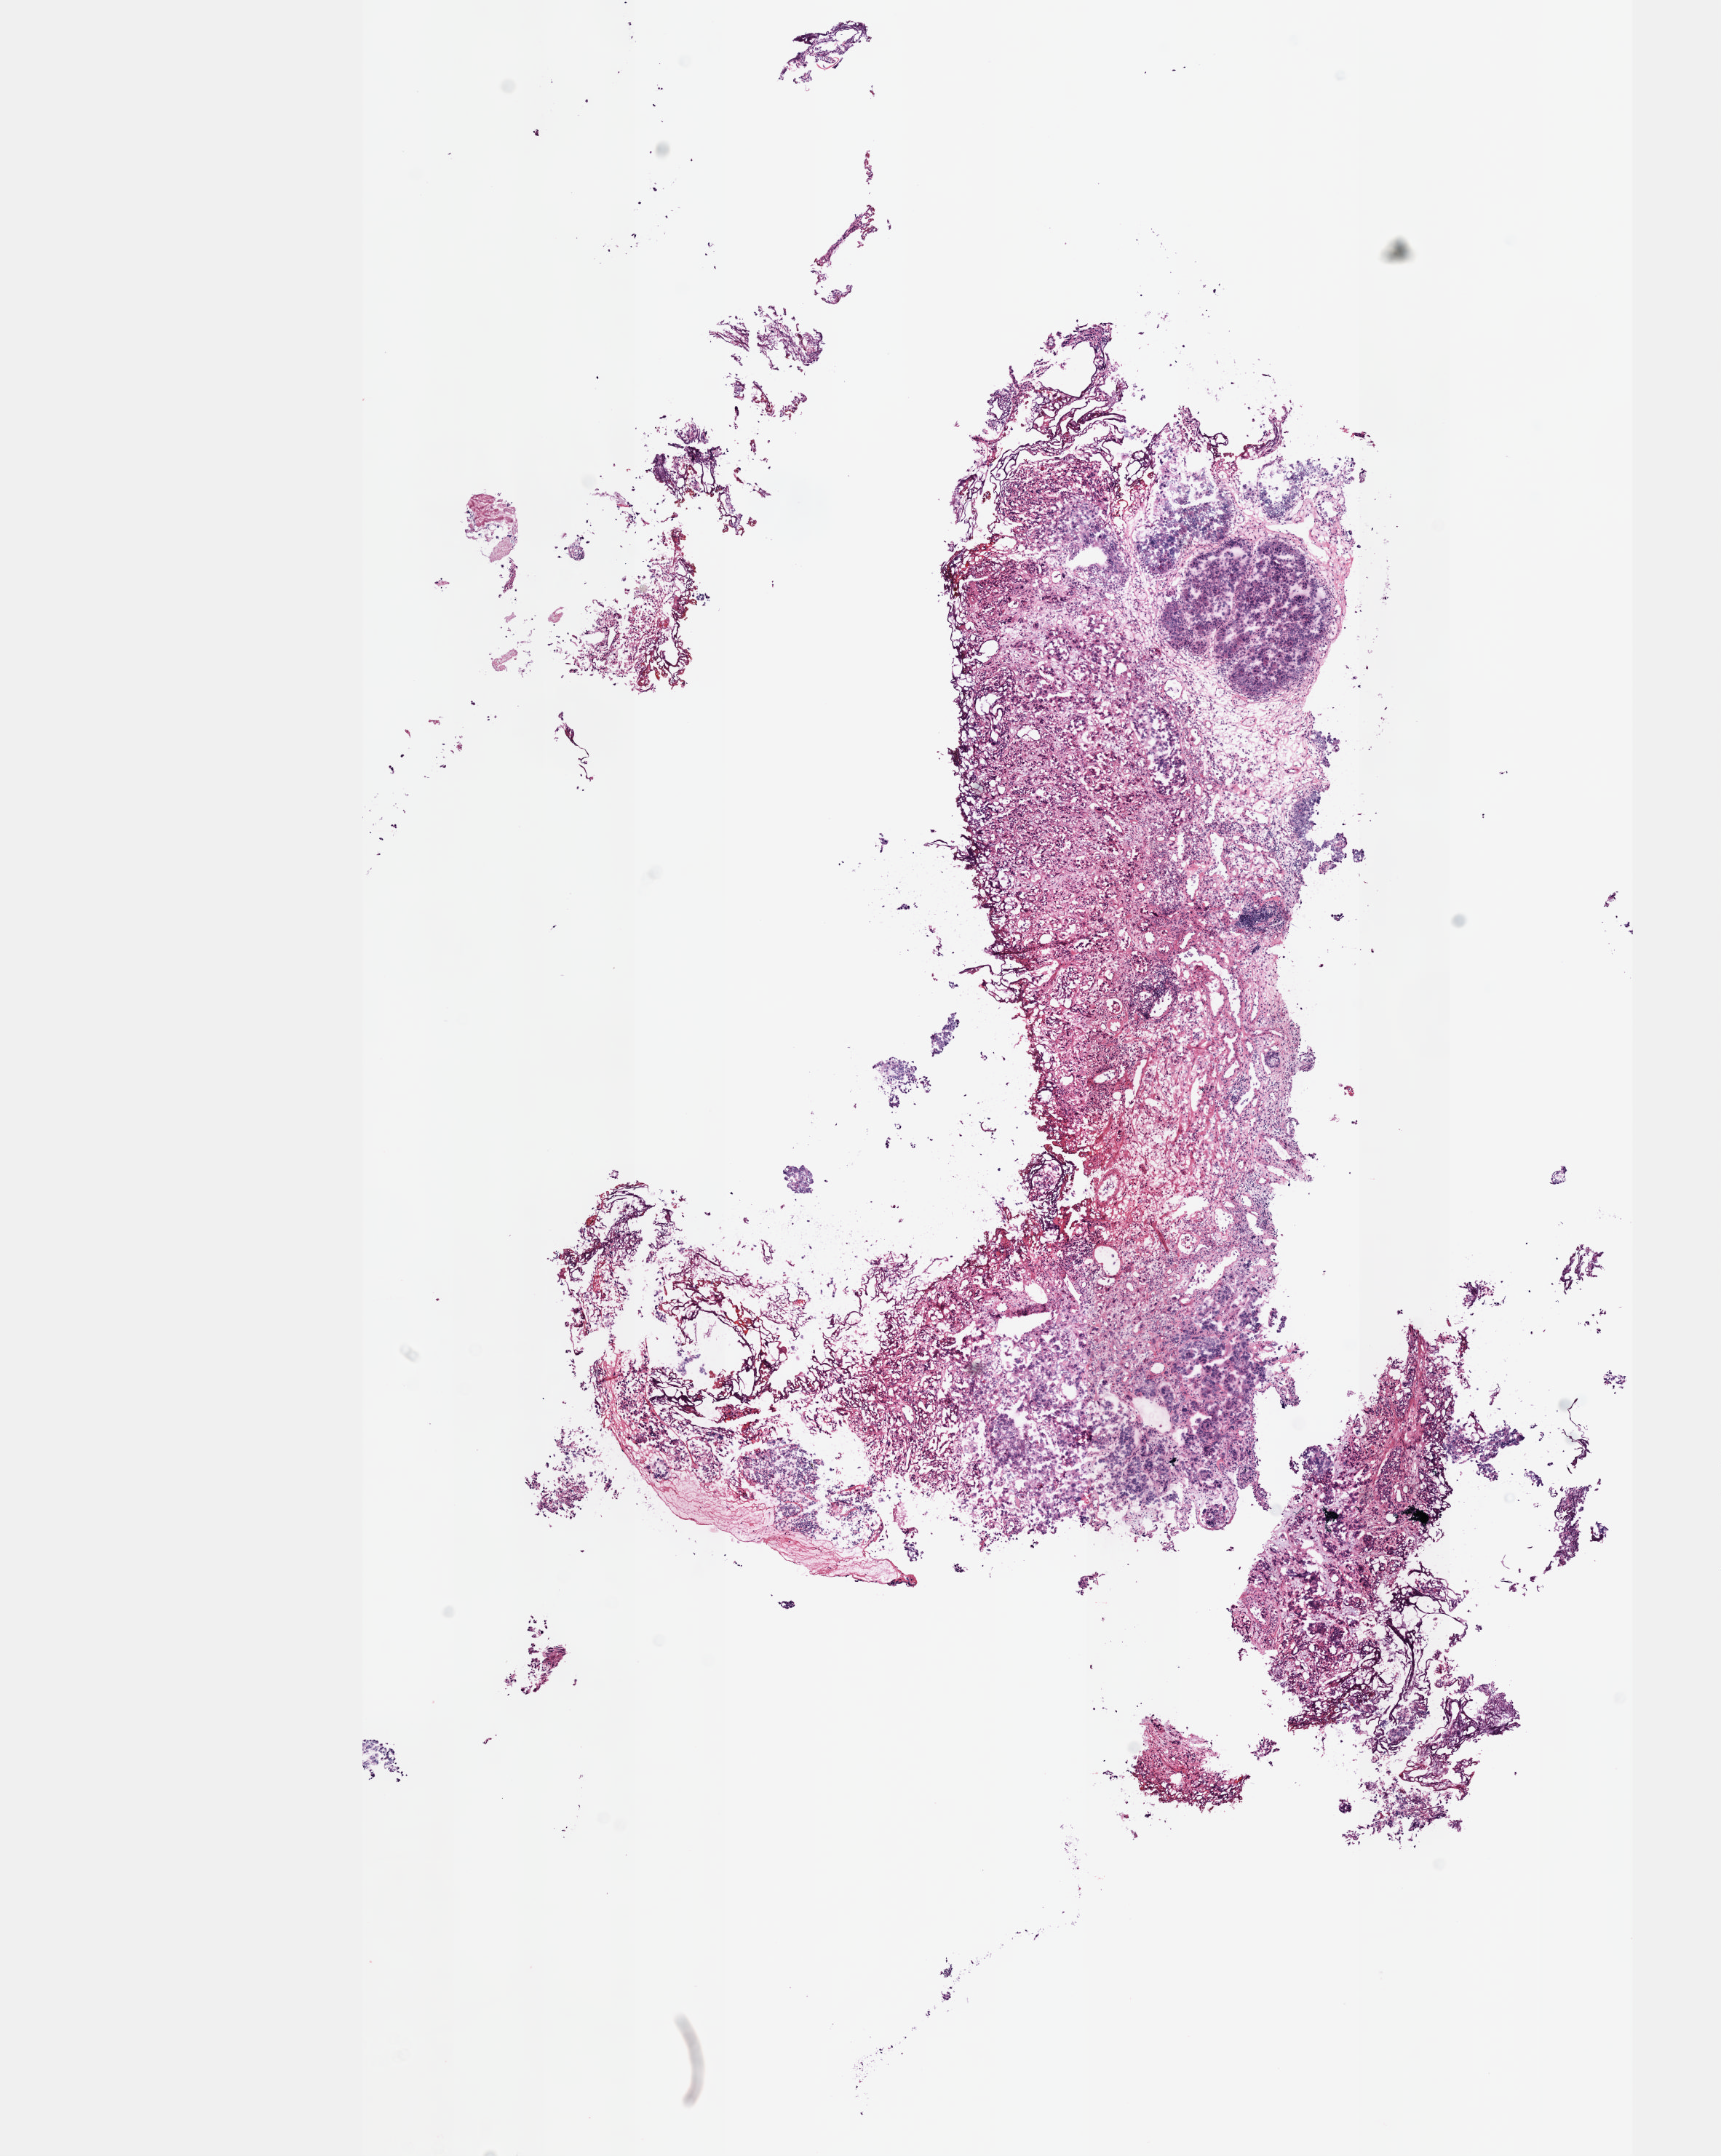
H&E-stained whole-slide image — a low-resolution overview of the entire scanned area, about 9.6 x 12.0 mm (from a 40x scan). Frozen section from the top of the tissue portion. Primary tumour sample from the bladder. Patient: male, age at initial diagnosis 64 years. Slide review estimates, as recorded: tumour cells 75%, tumour nuclei 75%, normal cells 0%, stromal cells 25%, necrosis 0%. Inflammatory infiltration, as recorded: lymphocyte infiltration 3%, monocyte infiltration 1%, neutrophil infiltration 5%.
• AJCC pathologic stage: II (7th edition)
• TNM: N0 M0
• diagnosis: Transitional cell carcinoma